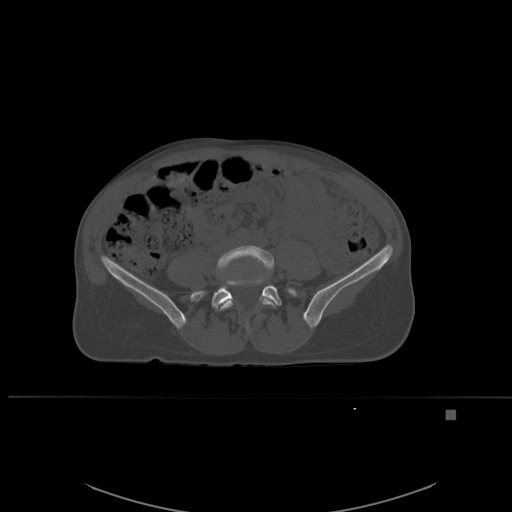
CT including the spine, one axial slice. Bone window (W 1800 / L 400 HU). 1.5 mm slice thickness. 512 × 512 image matrix. Female patient, age 45 years. From the clinical record (not read from this slice): primary cancer: lung.
Annotated regions visible in this slice (semi-automatically segmented with operator editing):
- L4 vertebra: bounding box (x1, y1, x2, y2) in pixels: (213, 245, 277, 333)
- L5 vertebra: (196, 279, 296, 308)